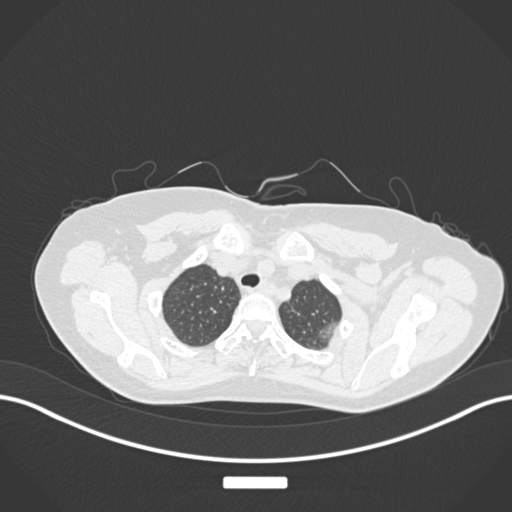
Chest CT, one axial slice. Position 152 of 181 along the scan axis. Lung window (W 1500 / L -600 HU). 1 mm slice thickness. 512 × 512 image matrix, field of view 400 × 400 mm. Female patient, age 58 years. Case-level facts recorded for this patient, not image findings: clinical TNM (as recorded): T1c N0 M0.
Outlined on this slice (rectangle marked by the reading radiologist):
- lung tumour (recorded histology: adenocarcinoma): box from (x=319, y=320) to (x=344, y=343) px